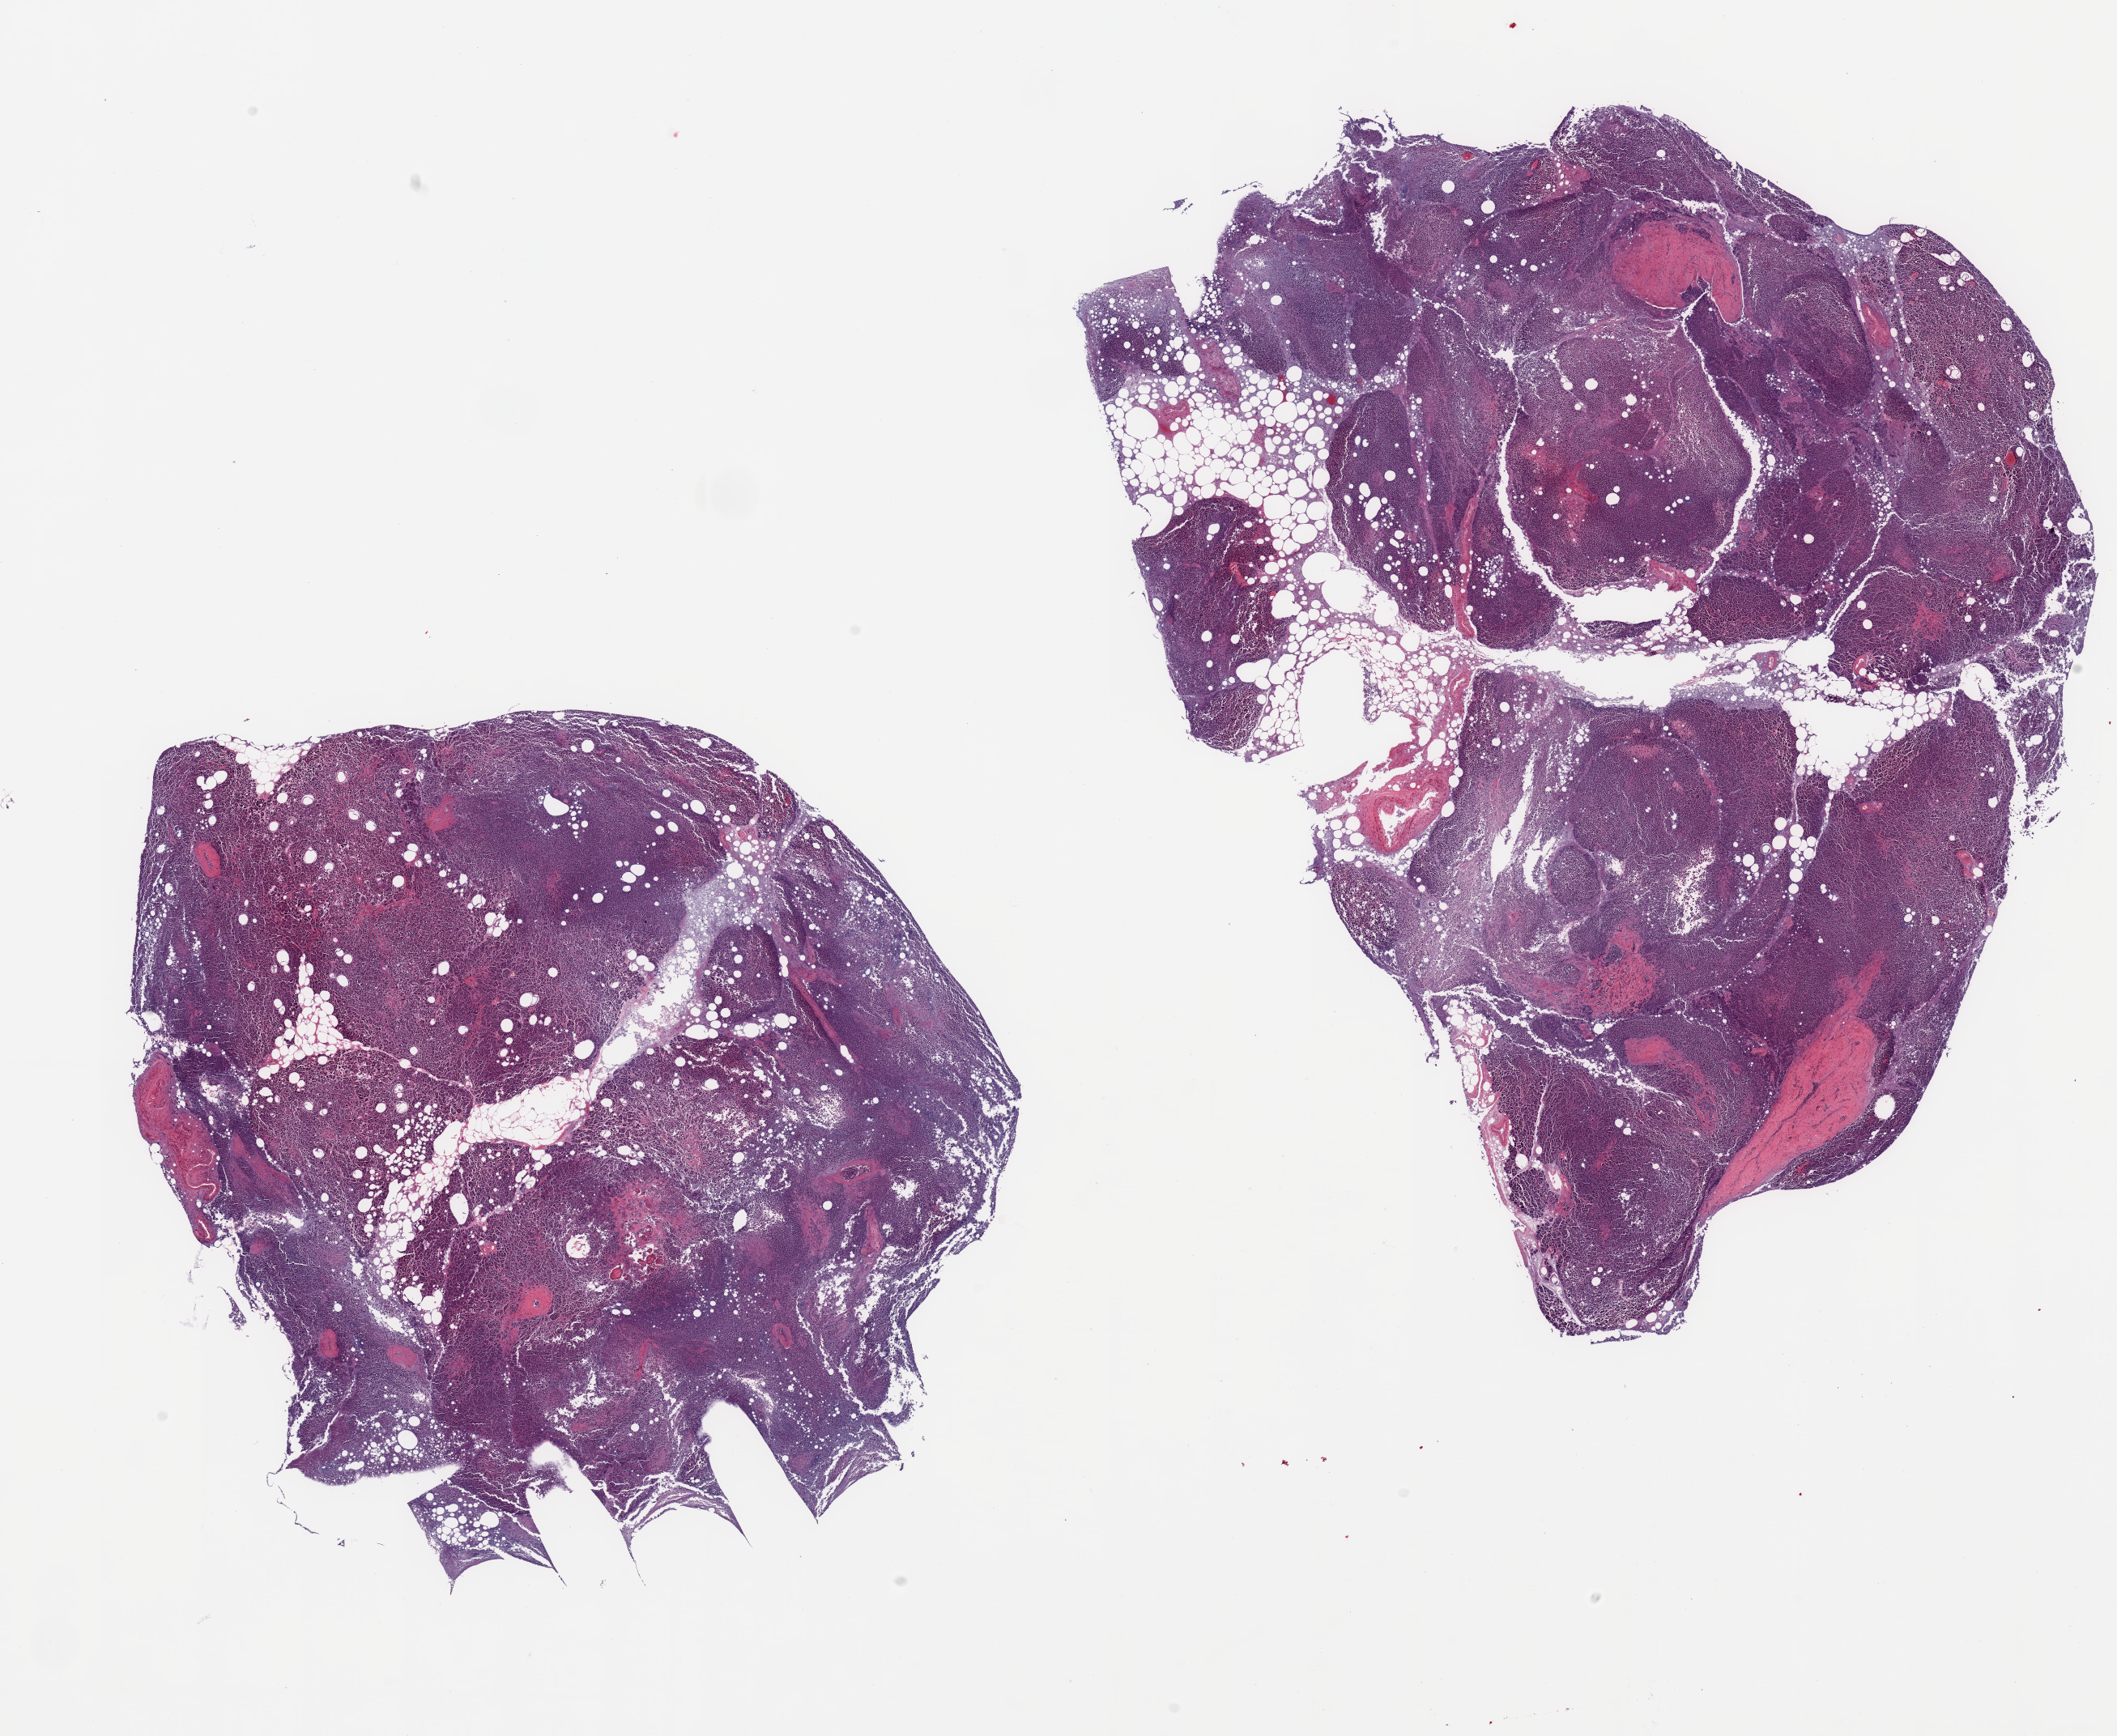
Digitized H&E-stained section — shown as a low-resolution overview of the whole scanned area (about 20.7 x 17.0 mm, from a 20x scan). PAXgene-fixed, paraffin-embedded tissue. Sampled site (target tissue): pancreas. Donor tissue sample. Donor: male.
* review note (as recorded): 2 pieces; marked autolysis of parenchyma and fat; periductal and interstitial fibrosis with focal accumulation of laminated, psammoma body-like material